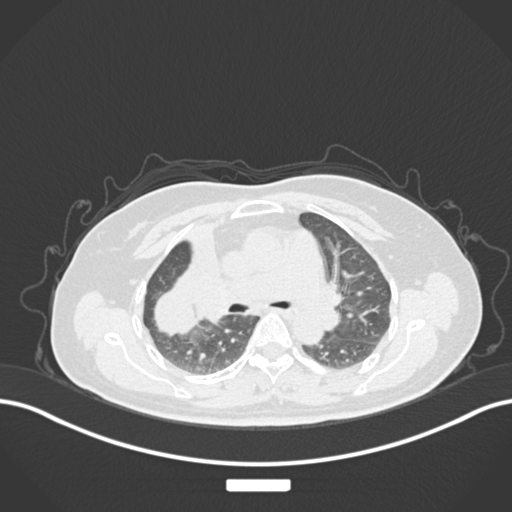
Chest CT, one axial slice; position 96 of 177 along the scan axis; 120 kVp; lung window (W 1500 / L -600 HU); 1 mm slice thickness; 512 × 512 image matrix, field of view 400 × 400 mm. Patient: female, 60 years. From the clinical record (not read from this slice): clinical TNM (as recorded): T3 N1 M1.
Annotated regions visible in this slice (bounding box drawn by a radiologist):
- lung tumour (recorded histology: adenocarcinoma): bounding box <125,250,213,342> (left, top, right, bottom; pixels)